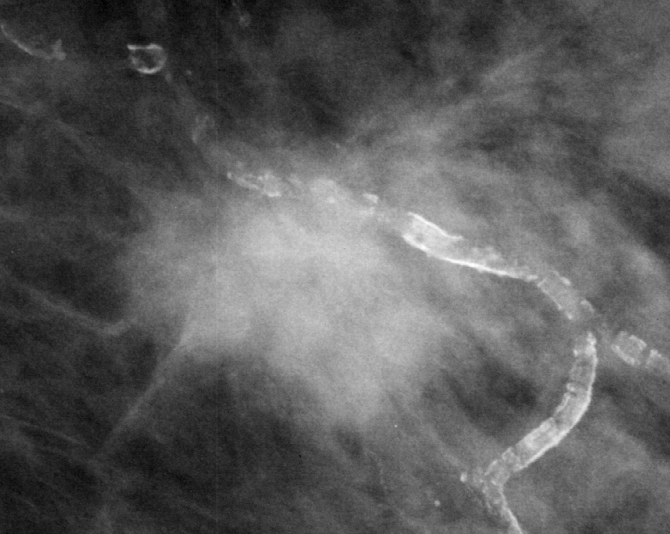
Region of interest cut from a scanned film mammogram (one marked finding); left breast; MLO view.
Marked abnormality: mass, shape oval, margins spiculated; BI-RADS assessment category 5; pathology result (as recorded, not read from the image): malignant.